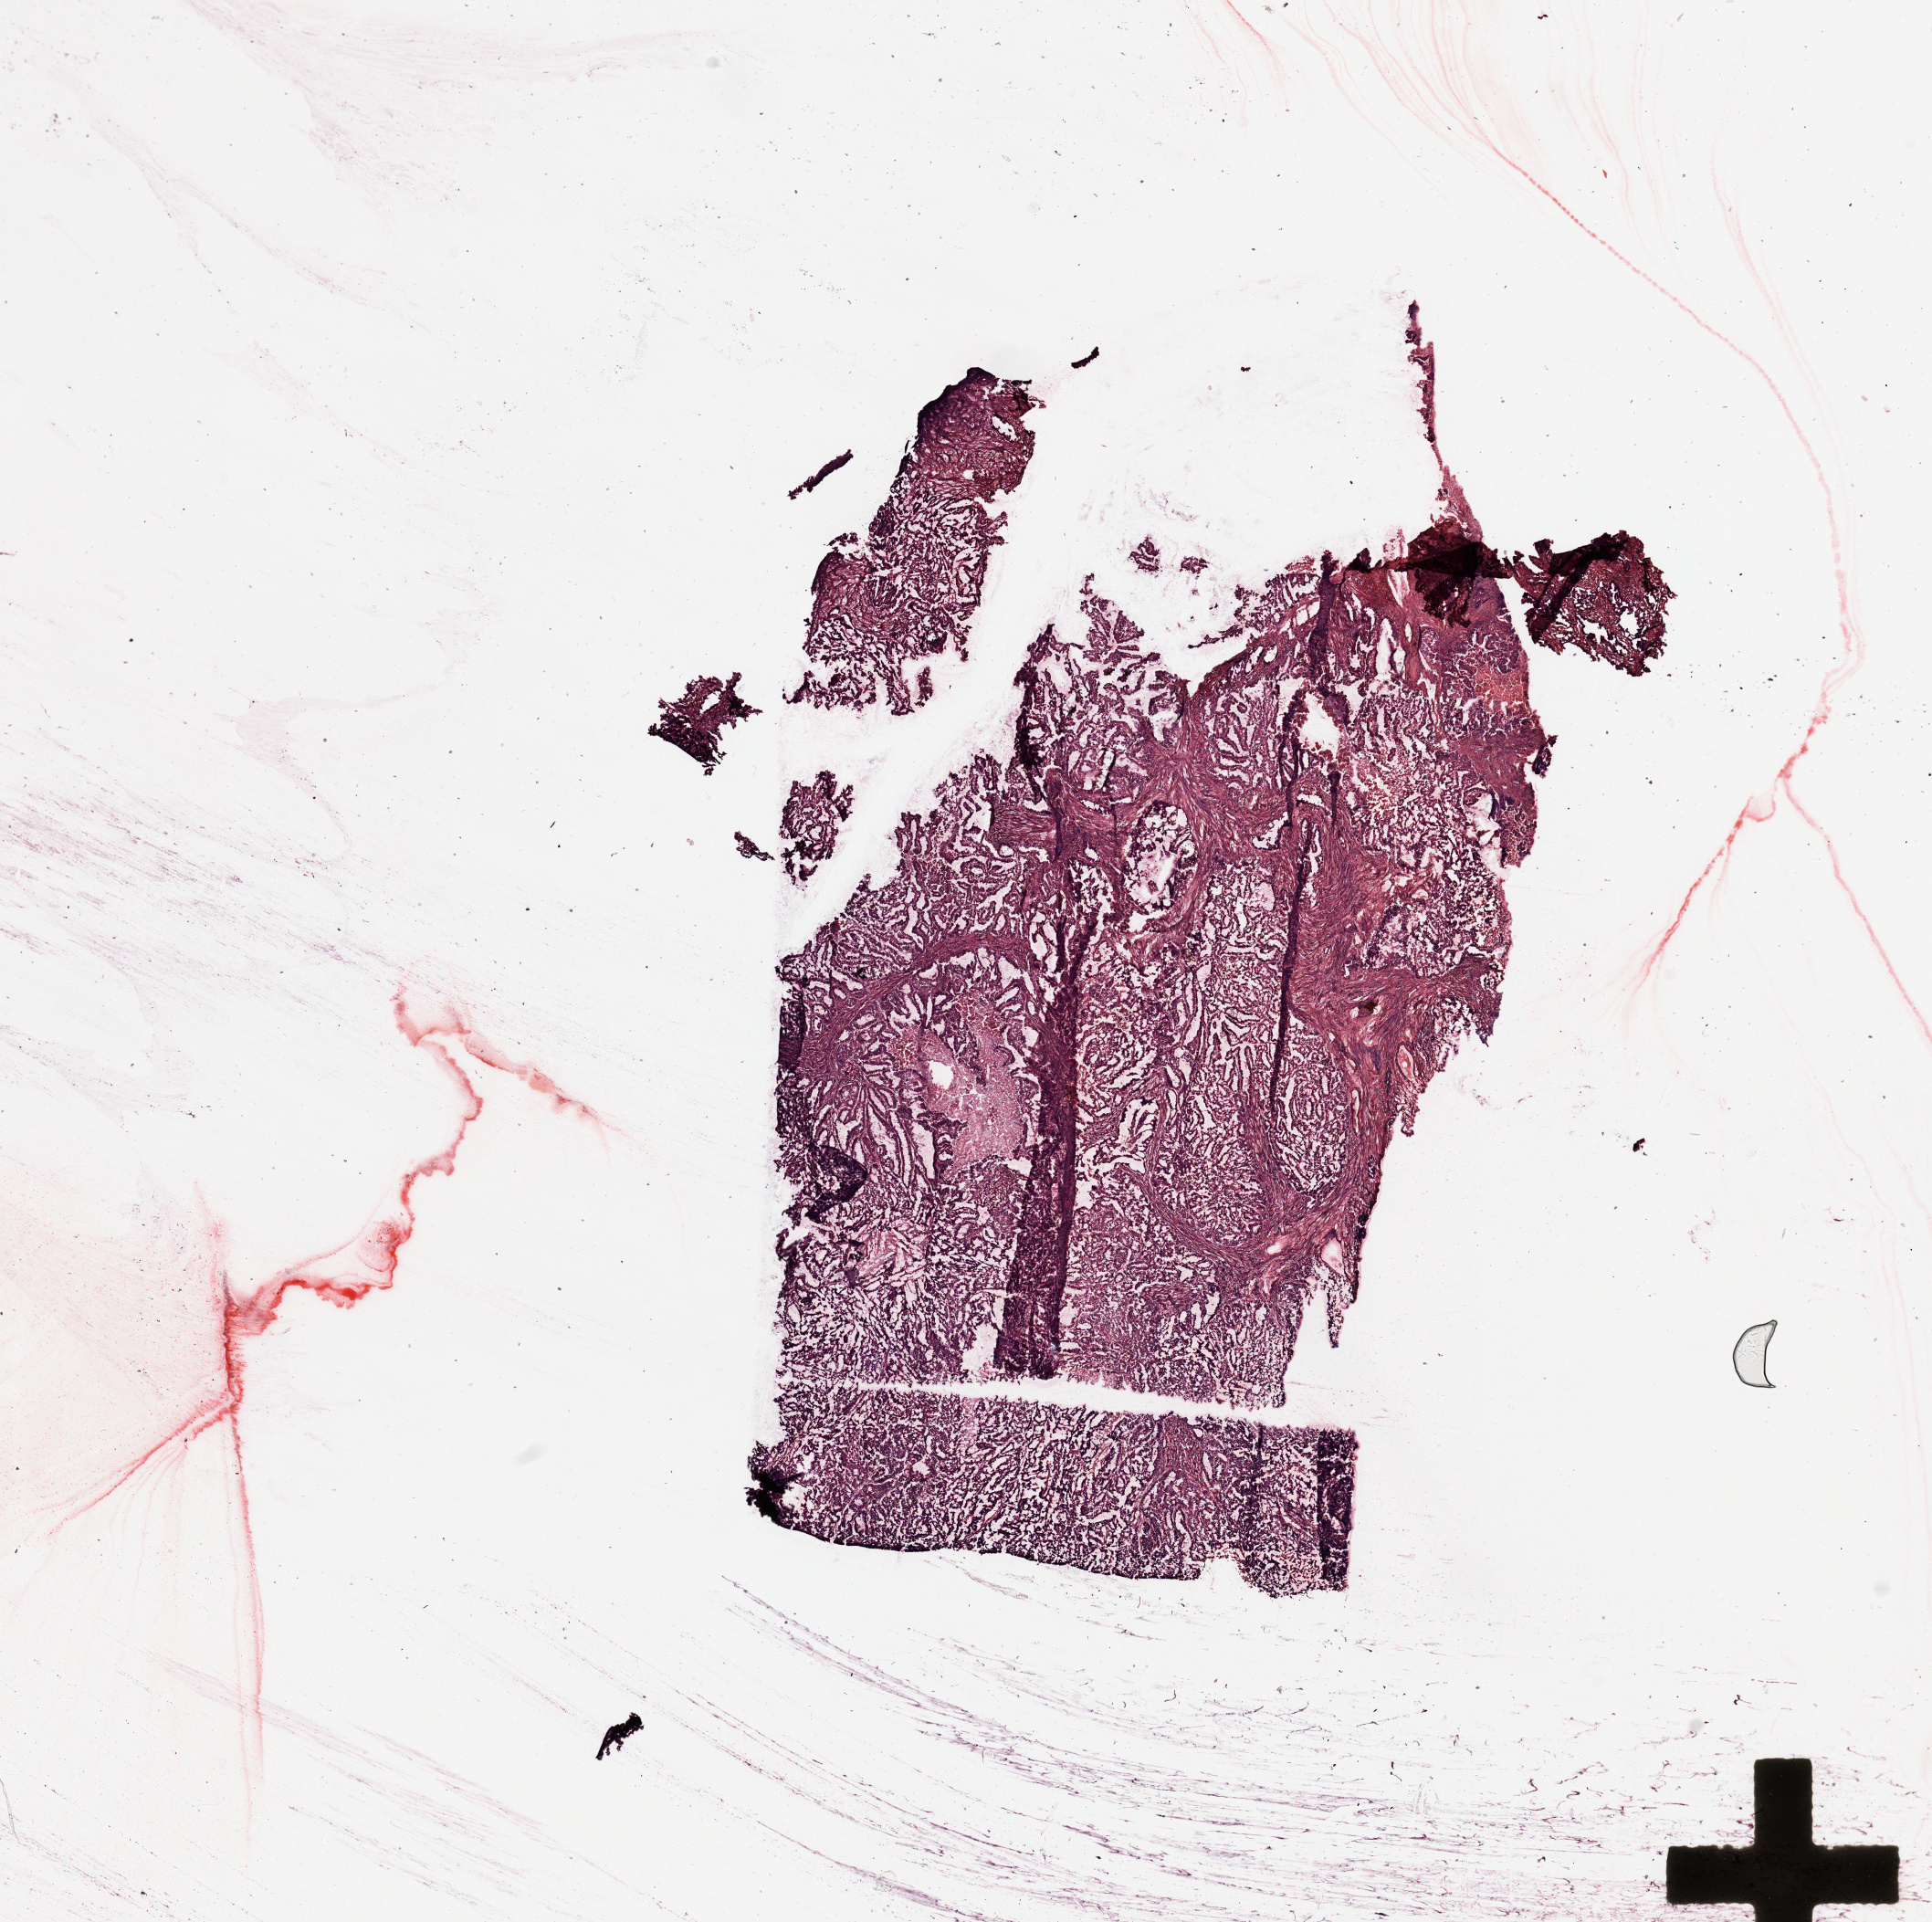
H&E whole-slide image, a low-resolution overview of the entire scanned area, about 16.7 x 16.6 mm (acquisition: 20x scan); uterus, tumour tissue. Patient: female, age 78 years.
Histologic diagnosis: Endometrioid adenocarcinoma, NOS.